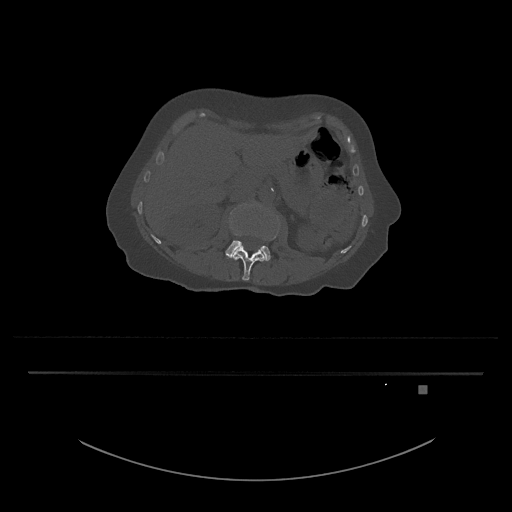
CT including the spine, one axial slice. Position 465 of 797 along the scan axis. 120 kVp. Bone window (W 1800 / L 400 HU). 0.5 mm slice thickness. 512 × 512 image matrix, field of view 500 × 500 mm. Female patient, age 57 years. Case-level facts recorded for this patient, not image findings: primary cancer: cervical.
Structures marked on this image (semi-automatically segmented with operator editing):
- L3 vertebra: box from (x=225, y=204) to (x=279, y=261) px